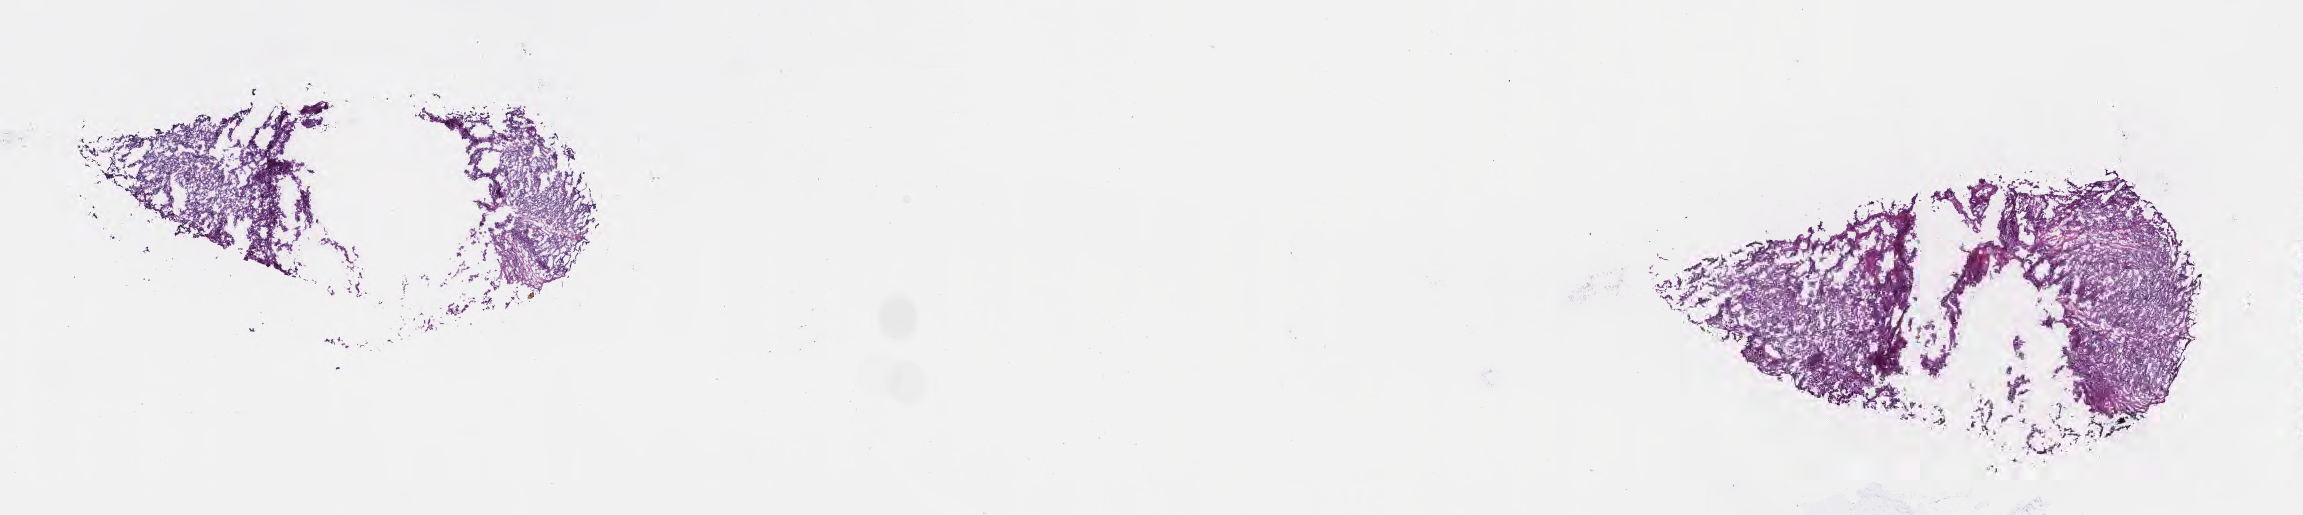
Whole-slide image, haematoxylin and eosin stain — a low-resolution overview of the entire scanned area, about 18.6 x 4.2 mm, frozen section, specimen: primary tumor, site: stomach. Male, age 56 years at initial diagnosis. Tumor grade: G3 (poorly differentiated). Pathologist review of this section (percent, as recorded): tumor cells 100%, tumor nuclei 85%, stromal cells 0%, necrosis 0%, normal cells 0%. Infiltration values recorded for this section: lymphocyte infiltration 0%, monocyte infiltration 0%, neutrophil infiltration 0%.
AJCC pathologic stage: Stage IIIB. Section: top of the tissue portion. Histologic diagnosis: Adenocarcinoma, NOS.